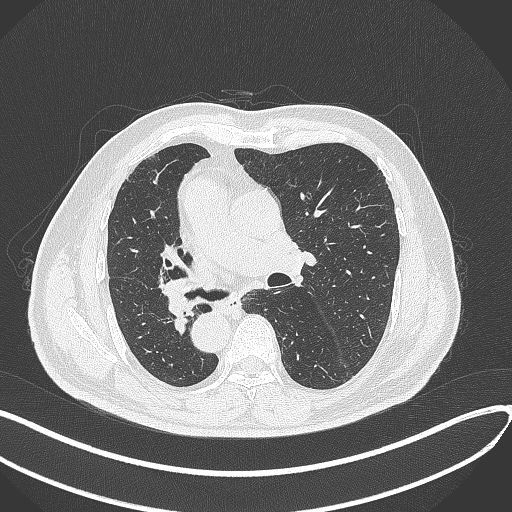
Chest CT, one axial slice; position 159 of 300 along the scan axis; reconstruction kernel B70f; lung window (W 1500 / L -600 HU); 512 × 512 image matrix. Male patient, age 67 years. Case-level facts recorded for this patient, not image findings: clinical TNM (as recorded): T2a N0 M0.
Structures marked on this image (bounding box drawn by a radiologist):
- lung tumour (recorded histology: squamous cell carcinoma): bounding box <152,280,201,317> (left, top, right, bottom; pixels)